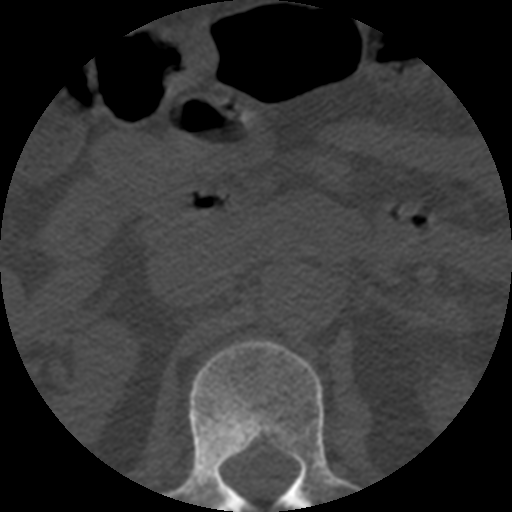
CT including the spine, one axial slice; reconstruction kernel STANDARD; 120 kVp; bone window (W 1800 / L 400 HU); 1.25 mm slice thickness; 512 × 512 image matrix. Patient age 57 years. From the clinical record (not read from this slice): primary cancer: prostate.
Annotated regions visible in this slice (semi-automatically segmented with operator editing):
- L1 vertebra: box from (x=167, y=341) to (x=357, y=512) px